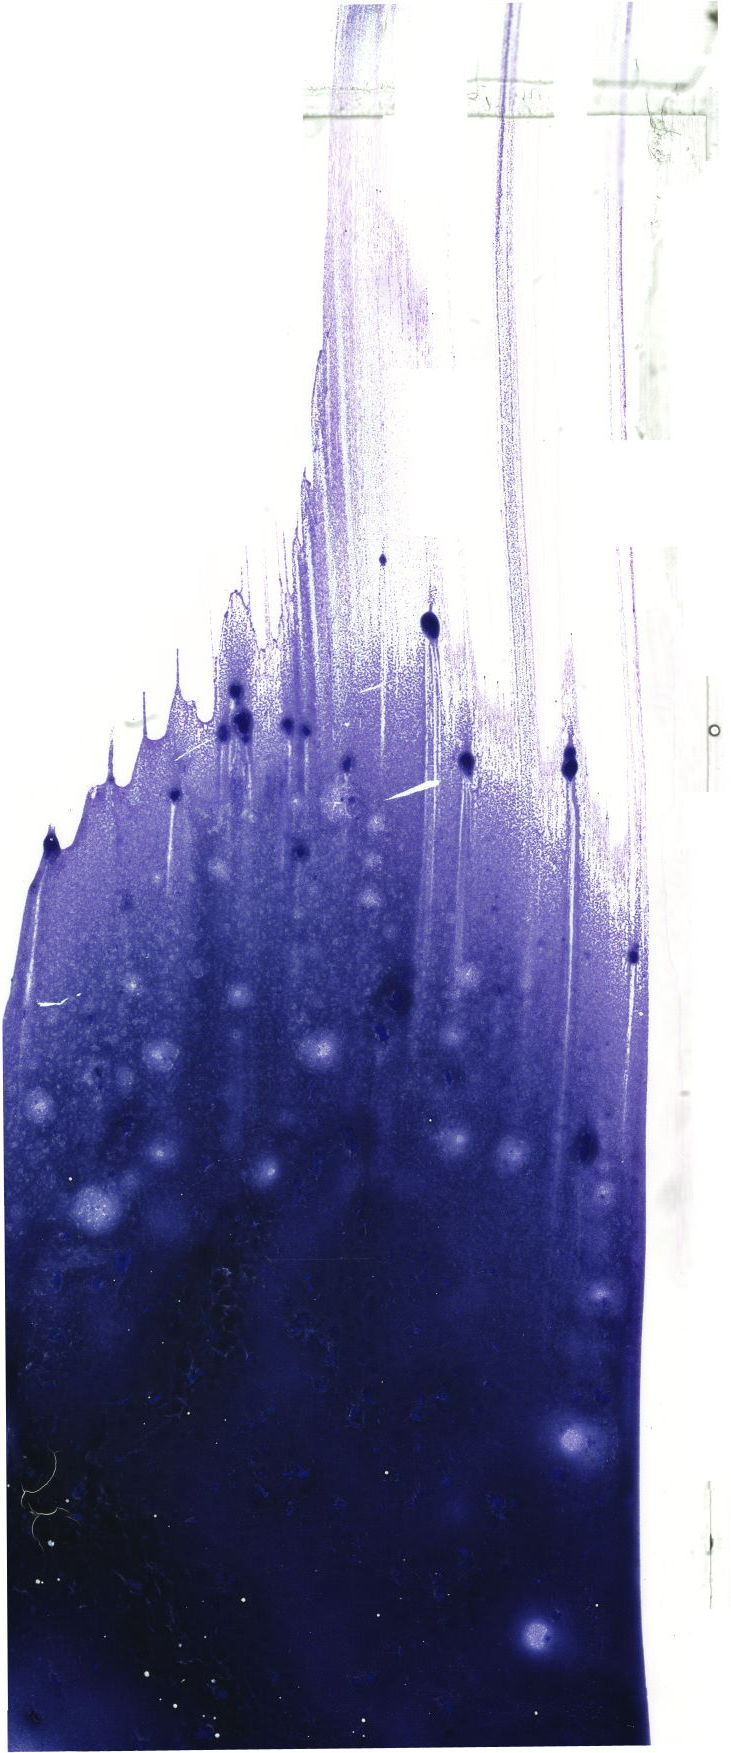
Whole-slide image of a May-Grünwald–Giemsa-stained bone marrow aspirate smear, shown as a low-resolution overview of the whole scanned area (about 20.7 x 49.7 mm). Patient sex: male.
Diagnosis: Chronic Phase Chronic Myeloid Leukemia, BCR-ABL1 Positive.